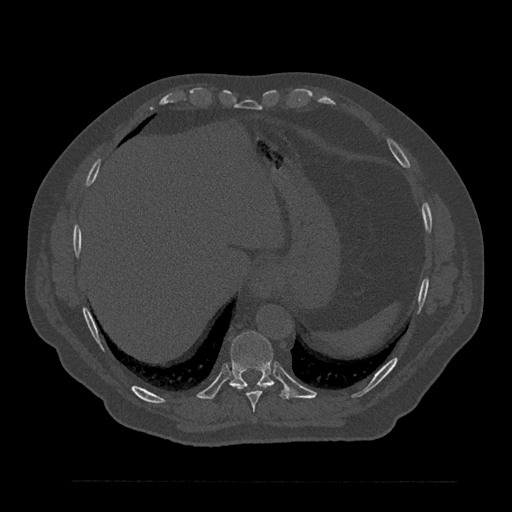
CT including the spine, one axial slice. Slice 376 of 797 in the series (ordered by position). Reconstruction kernel Br40s/3. 120 kVp. Bone window (W 1800 / L 400 HU). 0.5 mm slice thickness. 512 × 512 image matrix, field of view 430 × 430 mm. Patient: male, 61 years. Case-level facts recorded for this patient, not image findings: primary cancer: prostate.
Structures marked on this image (semi-automatically segmented with operator editing):
- T10 vertebra: bounding box [x1, y1, x2, y2] px = [229, 331, 287, 399]
- T9 vertebra: [235, 383, 268, 412]